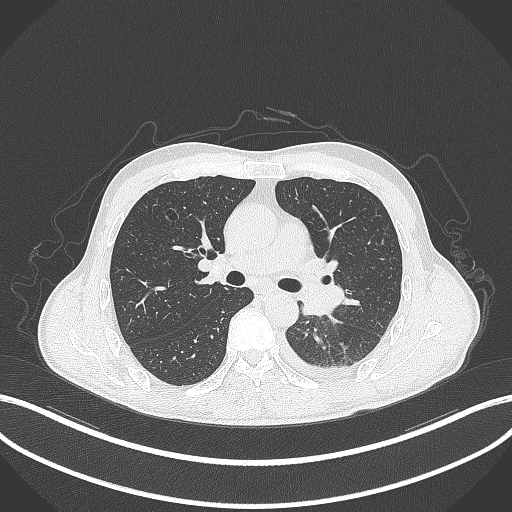
Chest CT, one axial slice; position 196 of 295 along the scan axis; 120 kVp; lung window (W 1500 / L -600 HU); 1 mm slice thickness; 512 × 512 image matrix, field of view 400 × 400 mm. Male patient, age 47 years. From the clinical record (not read from this slice): clinical TNM (as recorded): T3 N1 M1c.
Annotated regions visible in this slice (rectangle marked by the reading radiologist):
- lung tumour (recorded histology: small cell carcinoma): box from (x=298, y=279) to (x=343, y=321) px